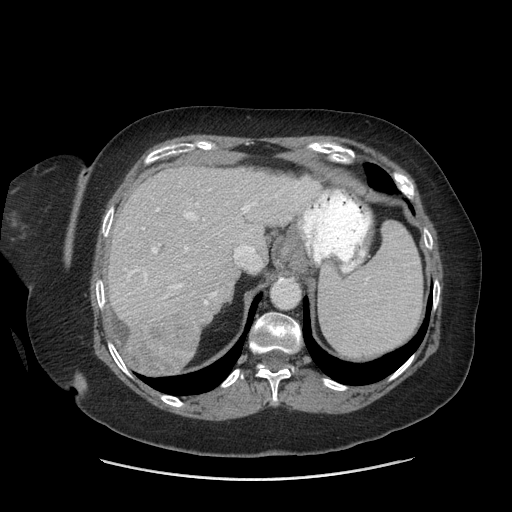
Contrast-enhanced abdominal CT (liver protocol), one axial slice; slice 53 of 69 in the series (ordered by position); soft-tissue window (W 400 / L 40 HU); 2.5 mm slice thickness; 512 × 512 image matrix, field of view 420 × 420 mm. From the clinical record (not read from this slice): diagnosis: hepatocellular carcinoma (patient treated with transarterial chemoembolisation; whether this scan precedes or follows treatment is not stated here); TNM stage (as recorded): Stage-IIIB; Child-Pugh class: A; tumour differentiation: moderately differentiated.
Outlined on this slice (semi-automatically segmented with operator editing):
- liver parenchyma outside the tumour (the mass and vessels are separate outlines, so this box may not span the whole liver): bounding box <106,166,320,372> (left, top, right, bottom; pixels)
- mass: <122,307,199,374>
- liver vessels: <128,189,296,305>